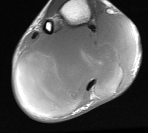
MRI of an extremity soft-tissue mass, one axial slice. Position 23 of 76 along the scan axis. MR volume resampled by the dataset authors to the PET/CT grid (not the native acquisition matrix). 3.27 mm slice thickness. 148 × 133 image matrix. Male patient. Case-level facts recorded for this patient, not image findings: histological type: liposarcoma - round cell; grade: high; site of the primary tumour: right calf.
Structures marked on this image (expert contour drawn on MRI and transferred to this co-registered scan by the dataset authors):
- gross tumour volume (mass): bounding box (x1, y1, x2, y2) in pixels: (13, 14, 139, 115)